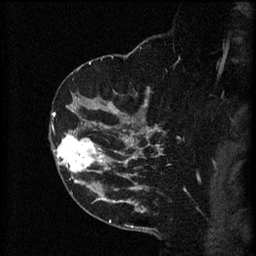
Breast MRI (dynamic contrast-enhanced), one sagittal slice; slice 39 of 60 in the series (ordered by position); 3 images stored at this slice position (order not interpretable as contrast timing); 1.5 T; TE 4.2 ms, TR 8.2 ms; 2 mm slice thickness; 256 × 256 image matrix, field of view 180 × 180 mm. Female patient, age 49 years.
Structures marked on this image (semi-automatically segmented with operator editing):
- analysis volume of interest (the breast-tissue region the enhancement analysis was run in; not a lesion): bounding box <49,126,105,175> (left, top, right, bottom; pixels)
- tumour enhancement mask (voxels above the 70 % enhancement threshold inside the analysis volume of interest): <53,134,105,173>